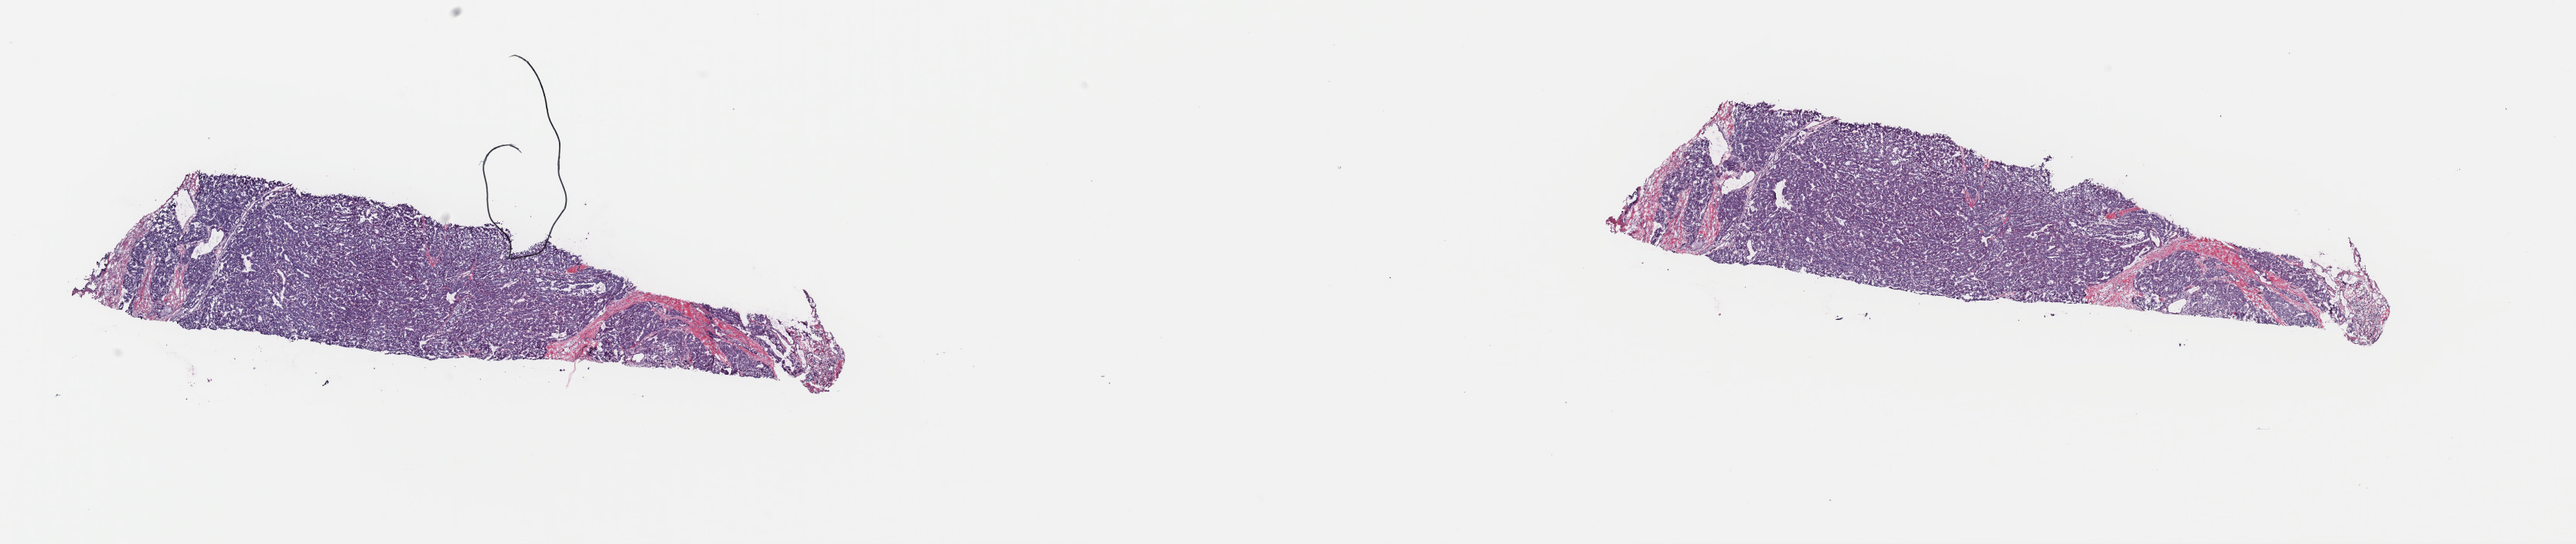
H&E-stained whole-slide image, low-resolution overview of the scanned area, about 26.3 x 5.6 mm (from a 40x scan). Frozen section from the top of the tissue portion. Thyroid, primary tumour sample. Patient: female, age at initial diagnosis 57 years. Composition of this section per pathologist review: tumour cells 95%, tumour nuclei 95%, normal cells 0%, stromal cells 5%, necrosis 0%. Inflammatory infiltration, as recorded: lymphocyte infiltration 0%, monocyte infiltration 0%, neutrophil infiltration 0%.
* laterality: left
* TNM: T2 N0 M0
* AJCC pathologic stage: II (7th edition)
* histologic diagnosis: Papillary adenocarcinoma, NOS (thyroid gland)